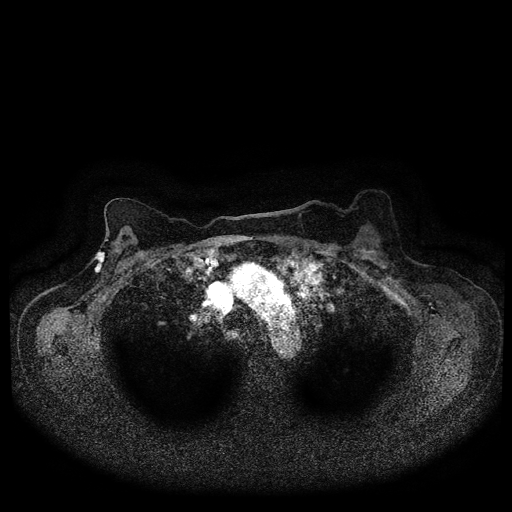
Breast MRI (dynamic contrast-enhanced, multi-phase), one axial slice. Dynamic contrast-enhanced series, time point 2 of 5 at this slice position (early post-contrast). 1.5 T. TE 2.7 ms, TR 5.4 ms. 512 × 512 image matrix, field of view 340 × 340 mm. Patient: female, 72 years.
Outlined on this slice (semi-automatic segmentation, software-assisted and operator-edited):
- breast lesion (labelled 'tumour' in the annotation; benign lesions carry a separate 'benign' label): bounding box <94,251,106,274> (left, top, right, bottom; pixels)